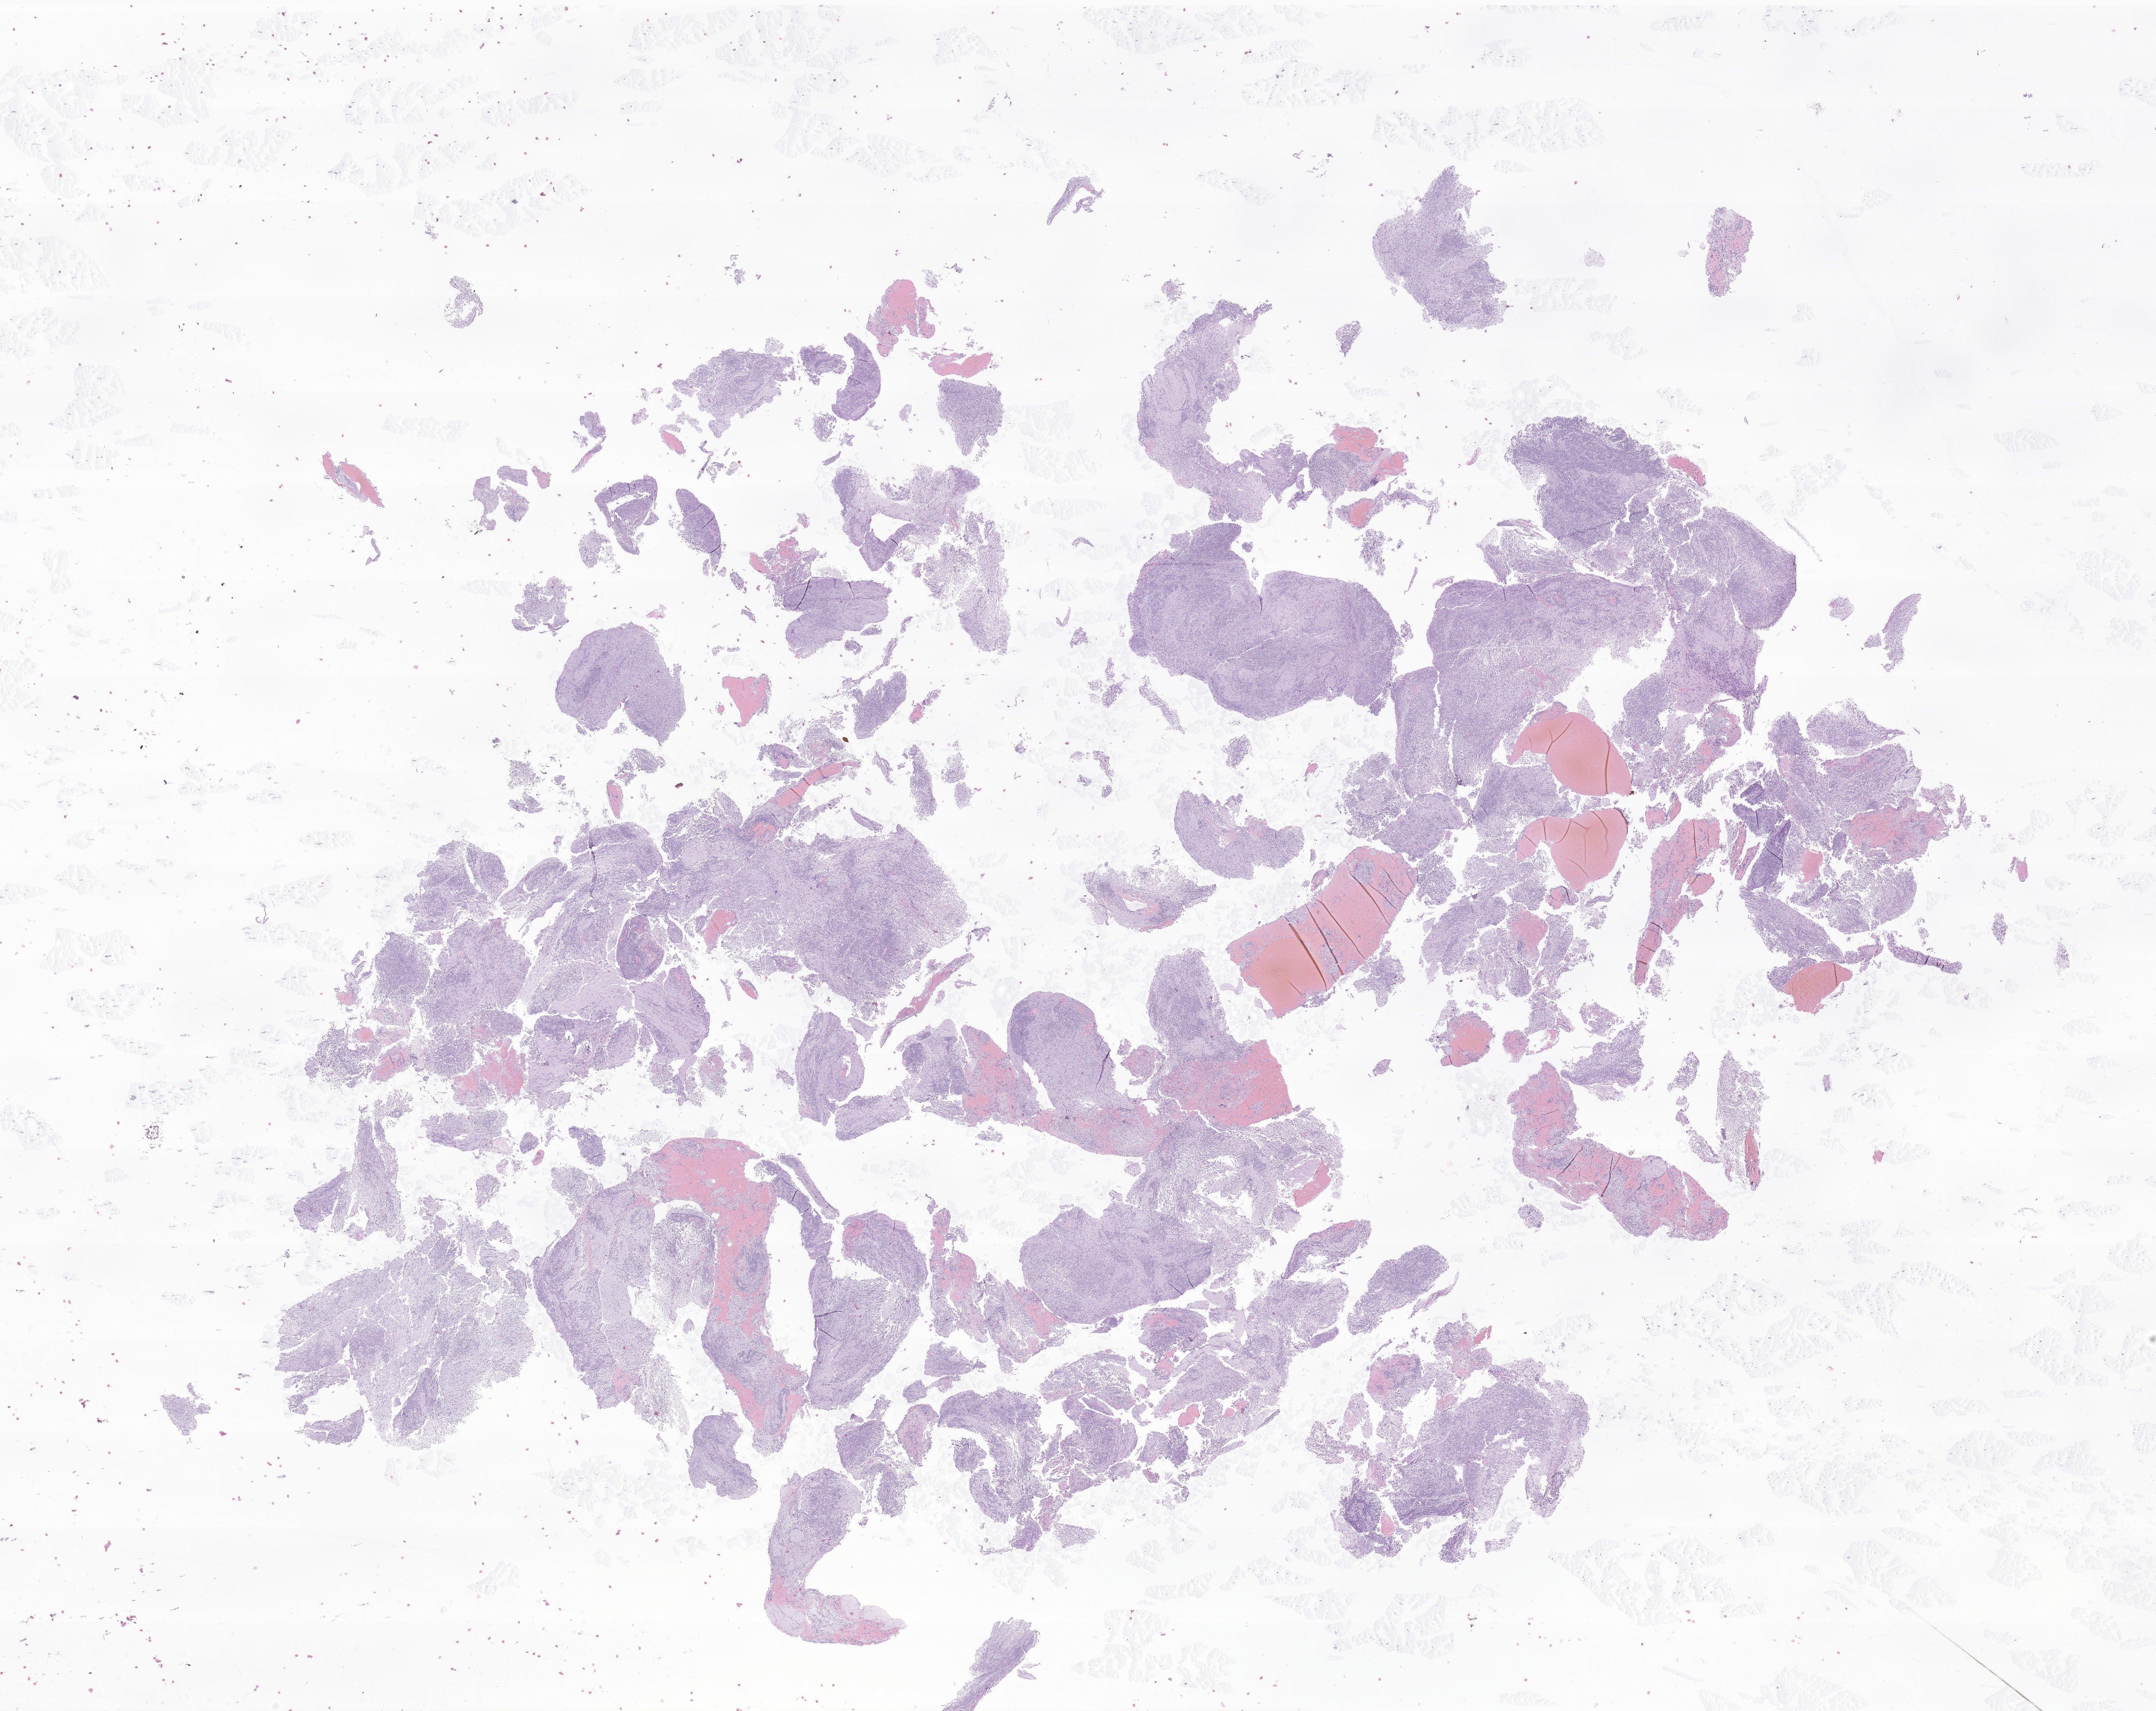
Hematoxylin and eosin (H&E) whole-slide image of tumor tissue from the brain stem, low-resolution overview of the scanned area, about 24.3 x 19.3 mm; formalin-fixed paraffin-embedded section. Male patient, age 584 days (about 1.6 years).
Diagnosis (ICD-O-3 morphology term): CNS embryonal tumor, NOS.